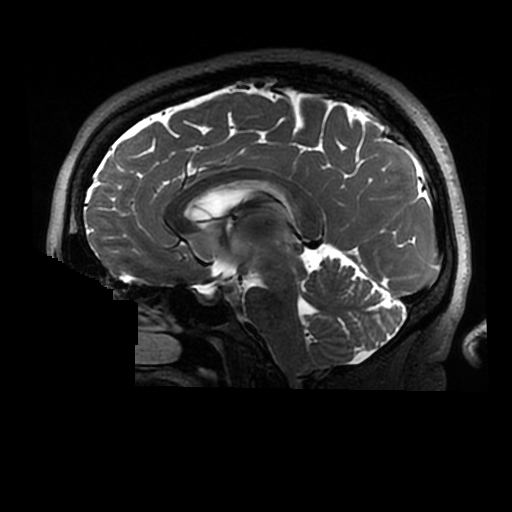
Brain MRI from a brain-tumour surgery series, one sagittal slice. 0.6 mm slice thickness. 512 × 512 image matrix, field of view 240 × 240 mm. From the clinical record (not read from this slice): histopathology: Astrocytoma; WHO grade: 2; IDH mutation: yes.
Outlined on this slice (expert manual segmentation):
- tumour: bounding box [x1, y1, x2, y2] px = [274, 208, 295, 242]